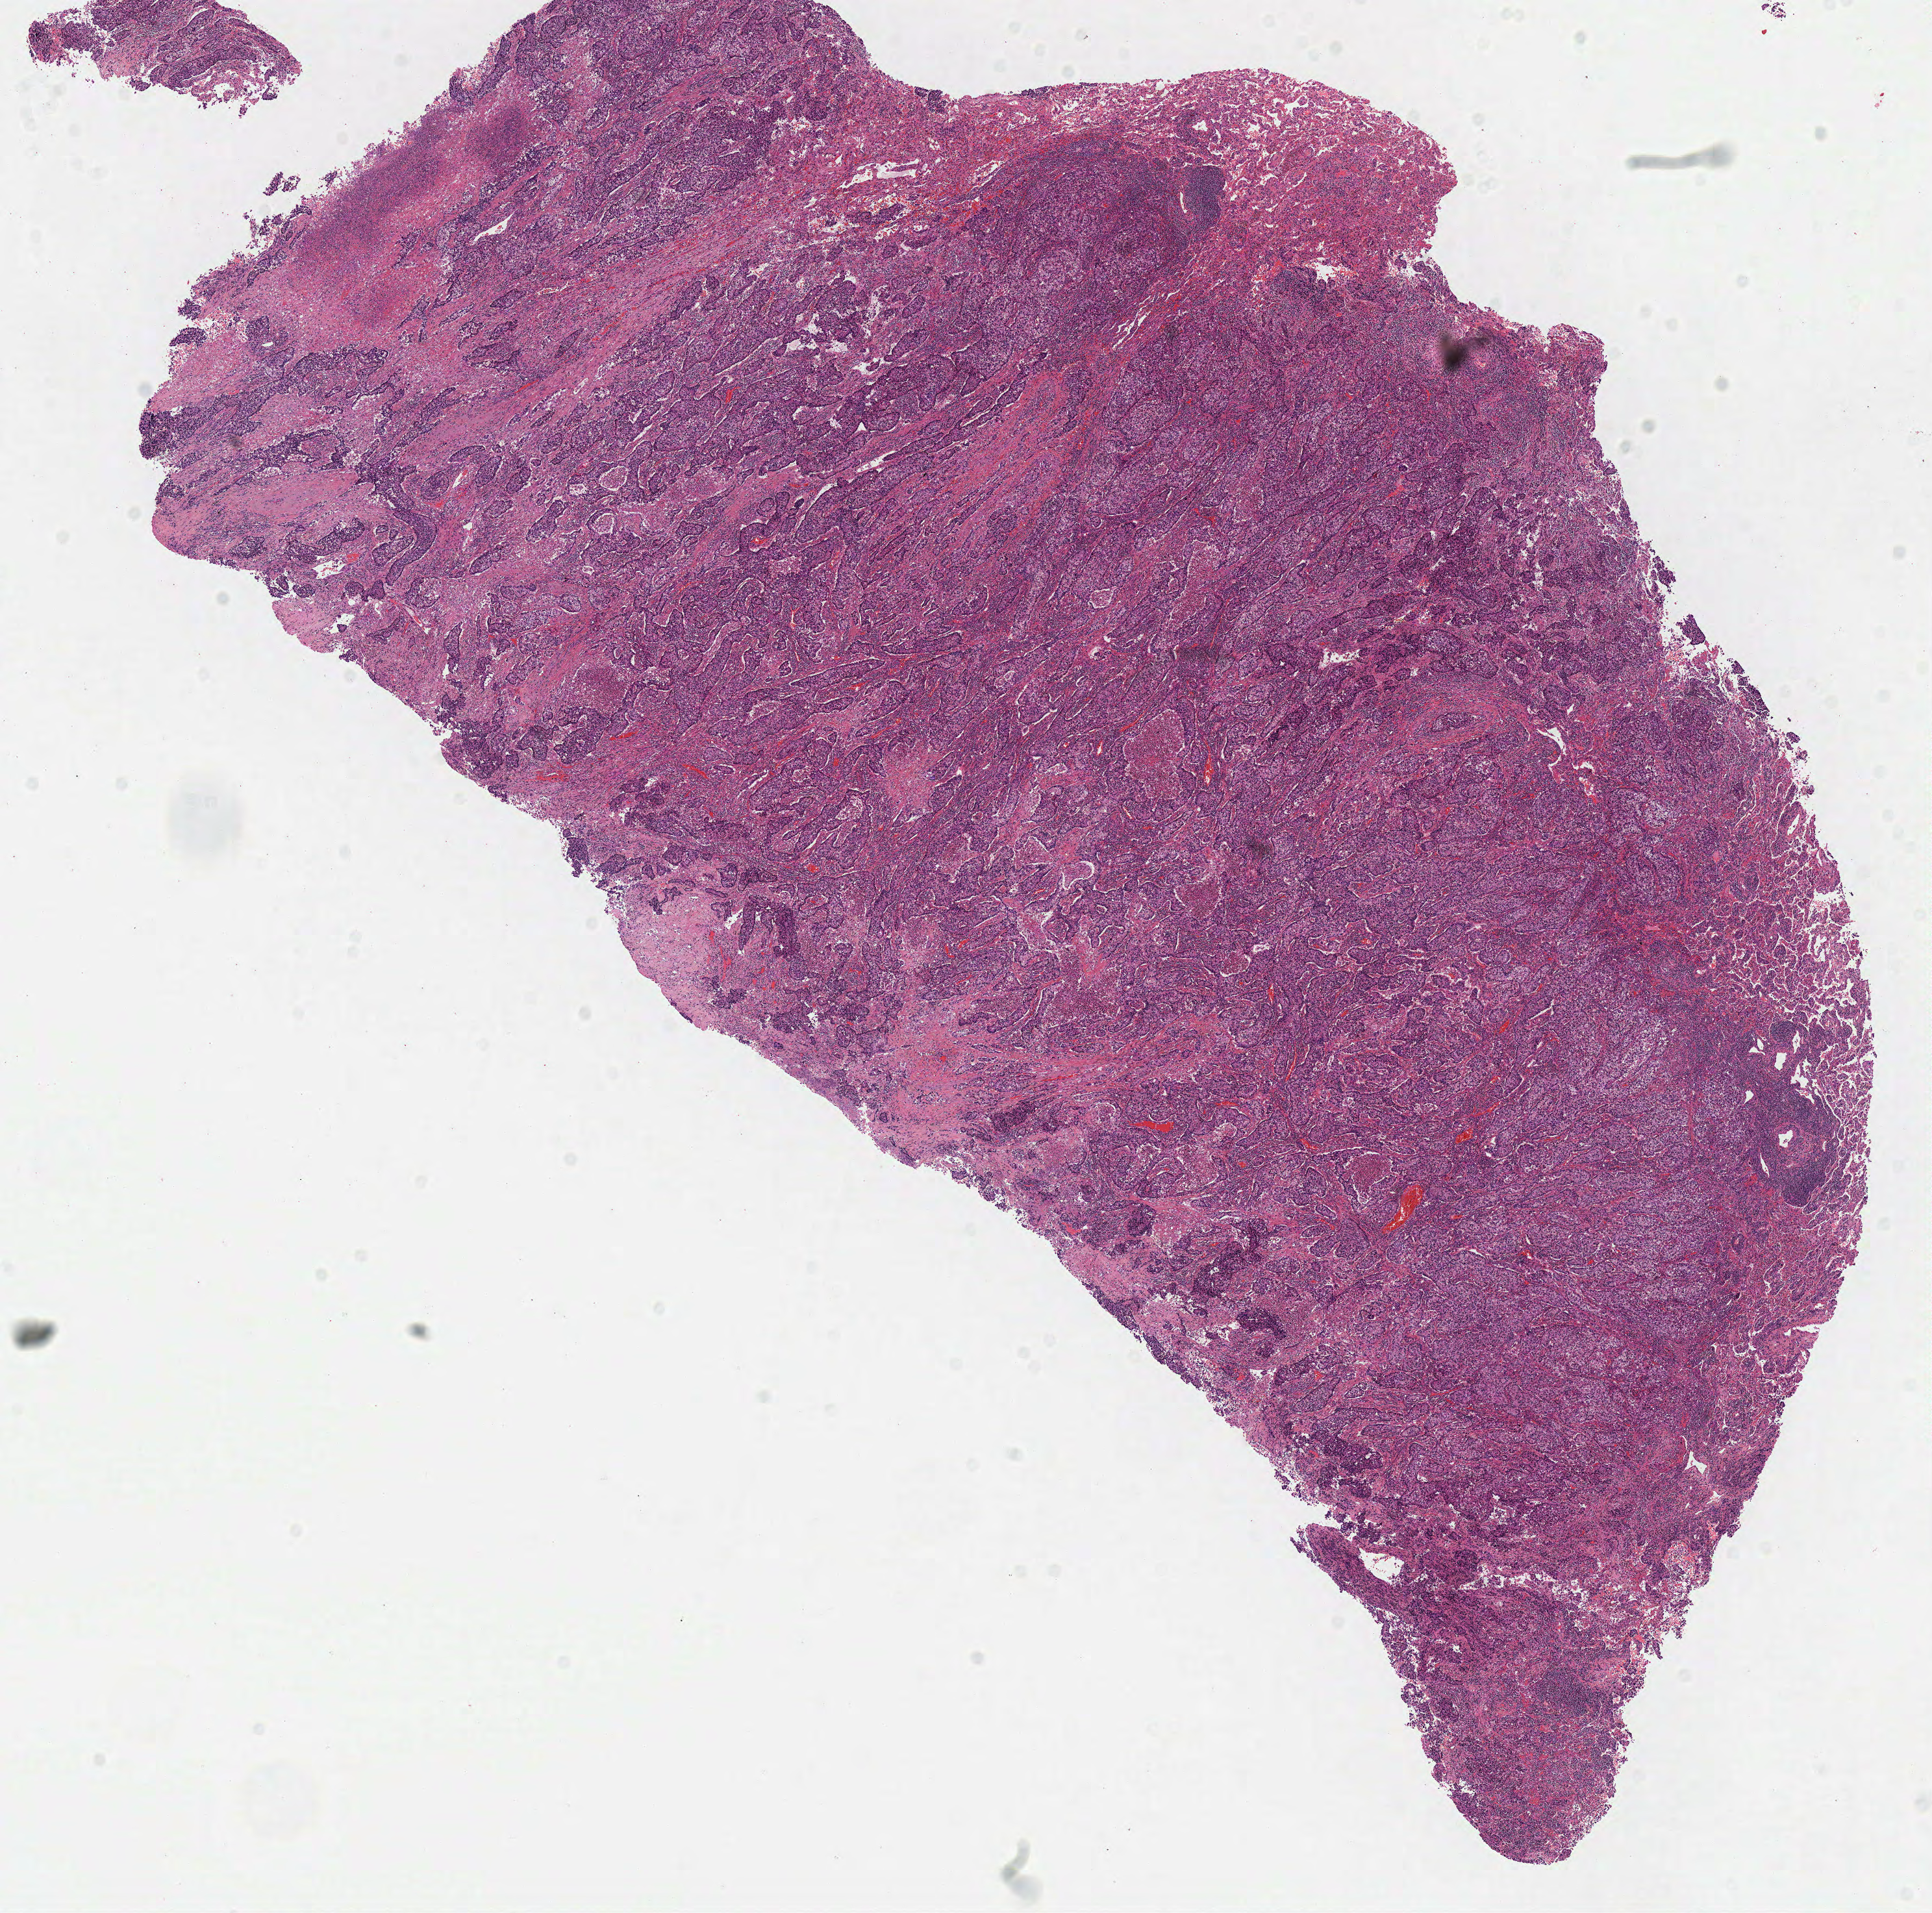
Whole-slide histology image, Hematoxylin and eosin (H&E) stained — low-resolution overview of the scanned area, about 11.7 x 11.6 mm (slide scanned at 40x); frozen section from the top of the tissue portion; sample: primary tumour, lung. Male patient; age at initial diagnosis 66 years. Pathologist review of this section (percent, as recorded): tumour cells 75%, tumour nuclei 80%, normal cells 0%, stromal cells 10%, necrosis 15%.
• diagnosis: Adenocarcinoma, NOS (middle lobe, lung)
• laterality: right
• TNM: T2 N0 MX
• AJCC pathologic stage: IB (5th edition)